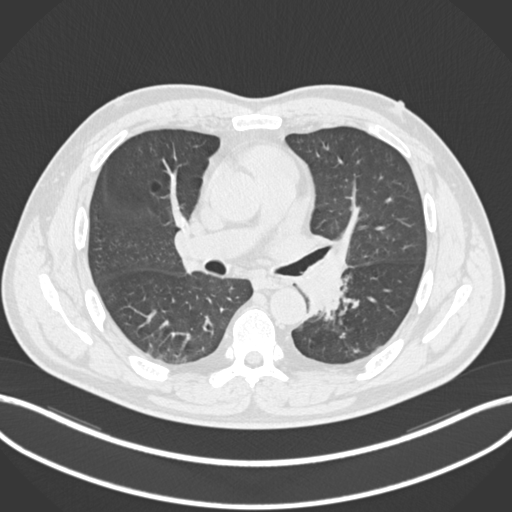
Chest CT, one axial slice. Slice 128 of 223 in the series (ordered by position). Reconstruction kernel B30f. 120 kVp. Lung window (W 1500 / L -600 HU). 512 × 512 image matrix, field of view 400 × 400 mm. Male patient, age 50 years. Case-level facts recorded for this patient, not image findings: clinical TNM (as recorded): T2a N3 M0.
Structures marked on this image (rectangle marked by the reading radiologist):
- lung tumour (recorded histology: squamous cell carcinoma): bounding box [x1, y1, x2, y2] px = [292, 239, 357, 320]